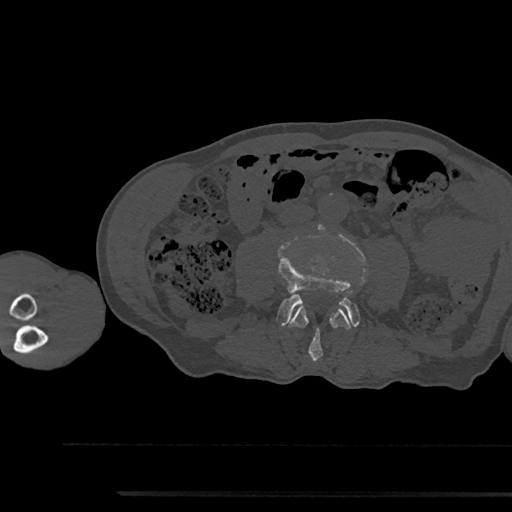
CT including the spine, one axial slice; slice 445 of 797 in the series (ordered by position); reconstruction kernel Br40s/3; bone window (W 1800 / L 400 HU); 0.5 mm slice thickness; 512 × 512 image matrix, field of view 367 × 367 mm. Male patient, age 79 years. From the clinical record (not read from this slice): primary cancer: prostate.
Structures marked on this image (semi-automatic segmentation, software-assisted and operator-edited):
- L3 vertebra: bounding box [x1, y1, x2, y2] px = [288, 304, 351, 361]
- L4 vertebra: [278, 252, 359, 326]